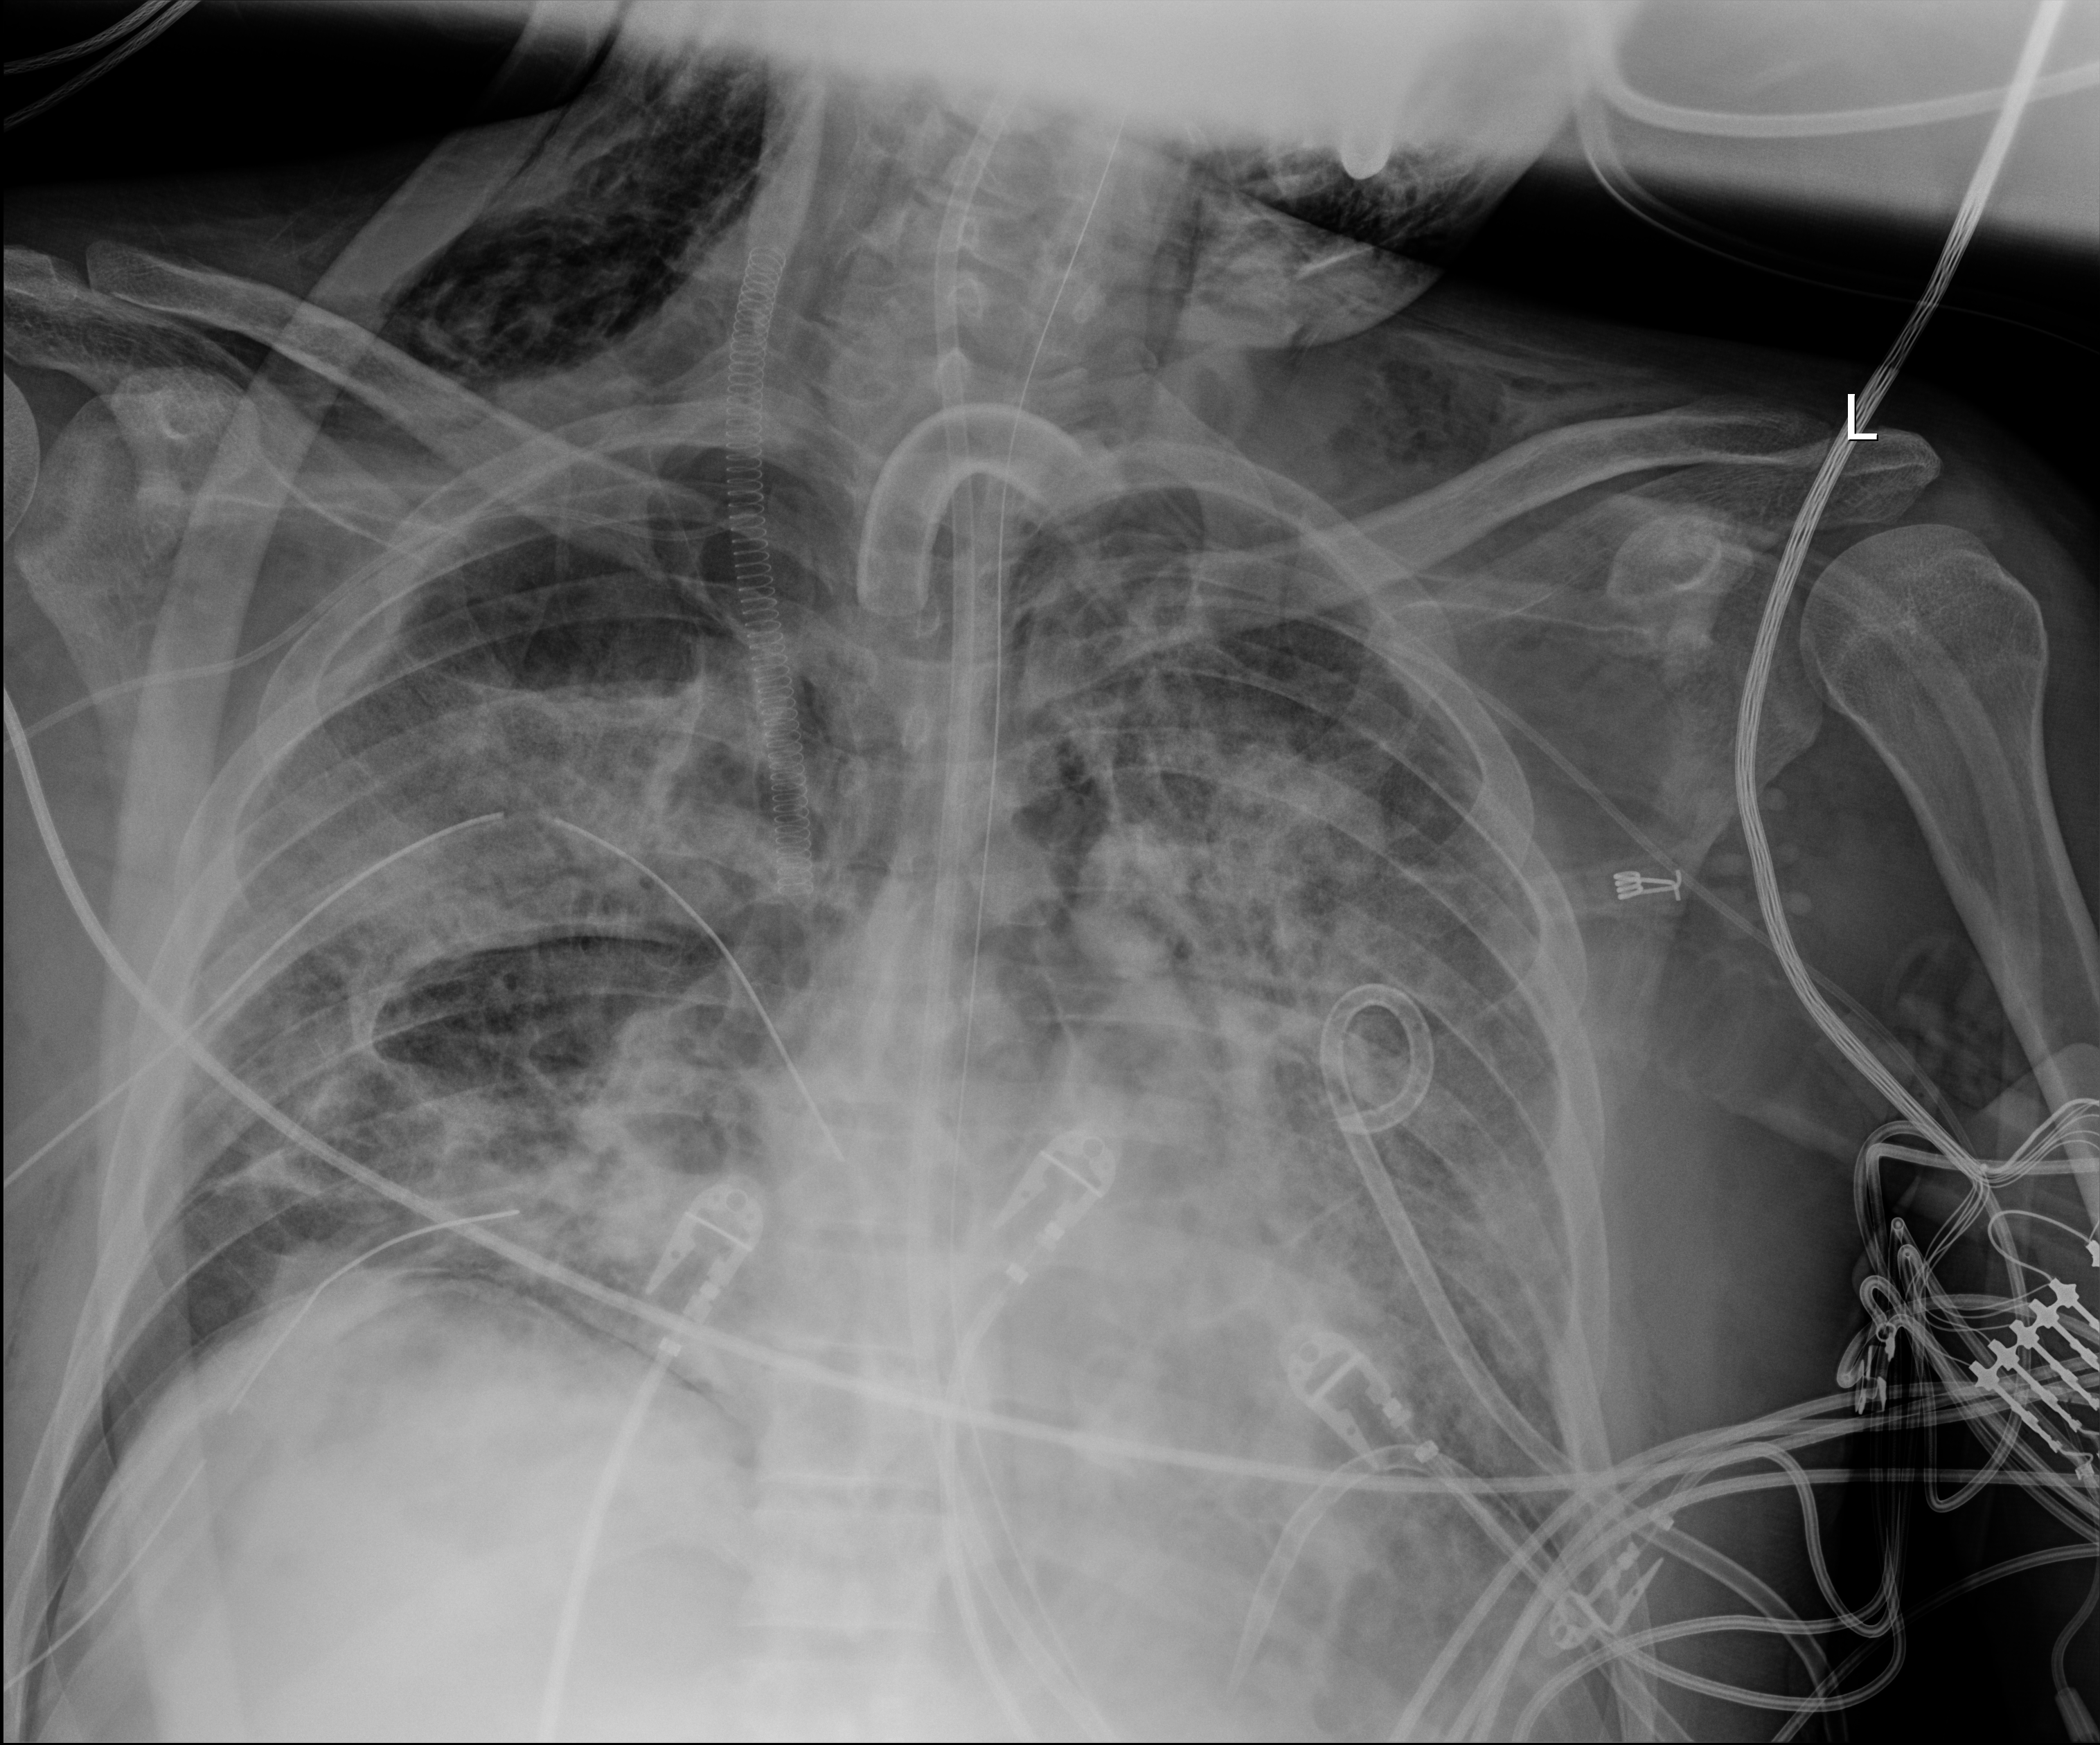
Chest radiograph; anteroposterior (AP) projection. Patient hospitalised with COVID-19, aged 18–59 years.
Admission-level facts for this patient (not findings on this image; timing relative to this image not recorded):
- mechanically ventilated during this hospital stay: yes
- length of hospital stay: 60 days